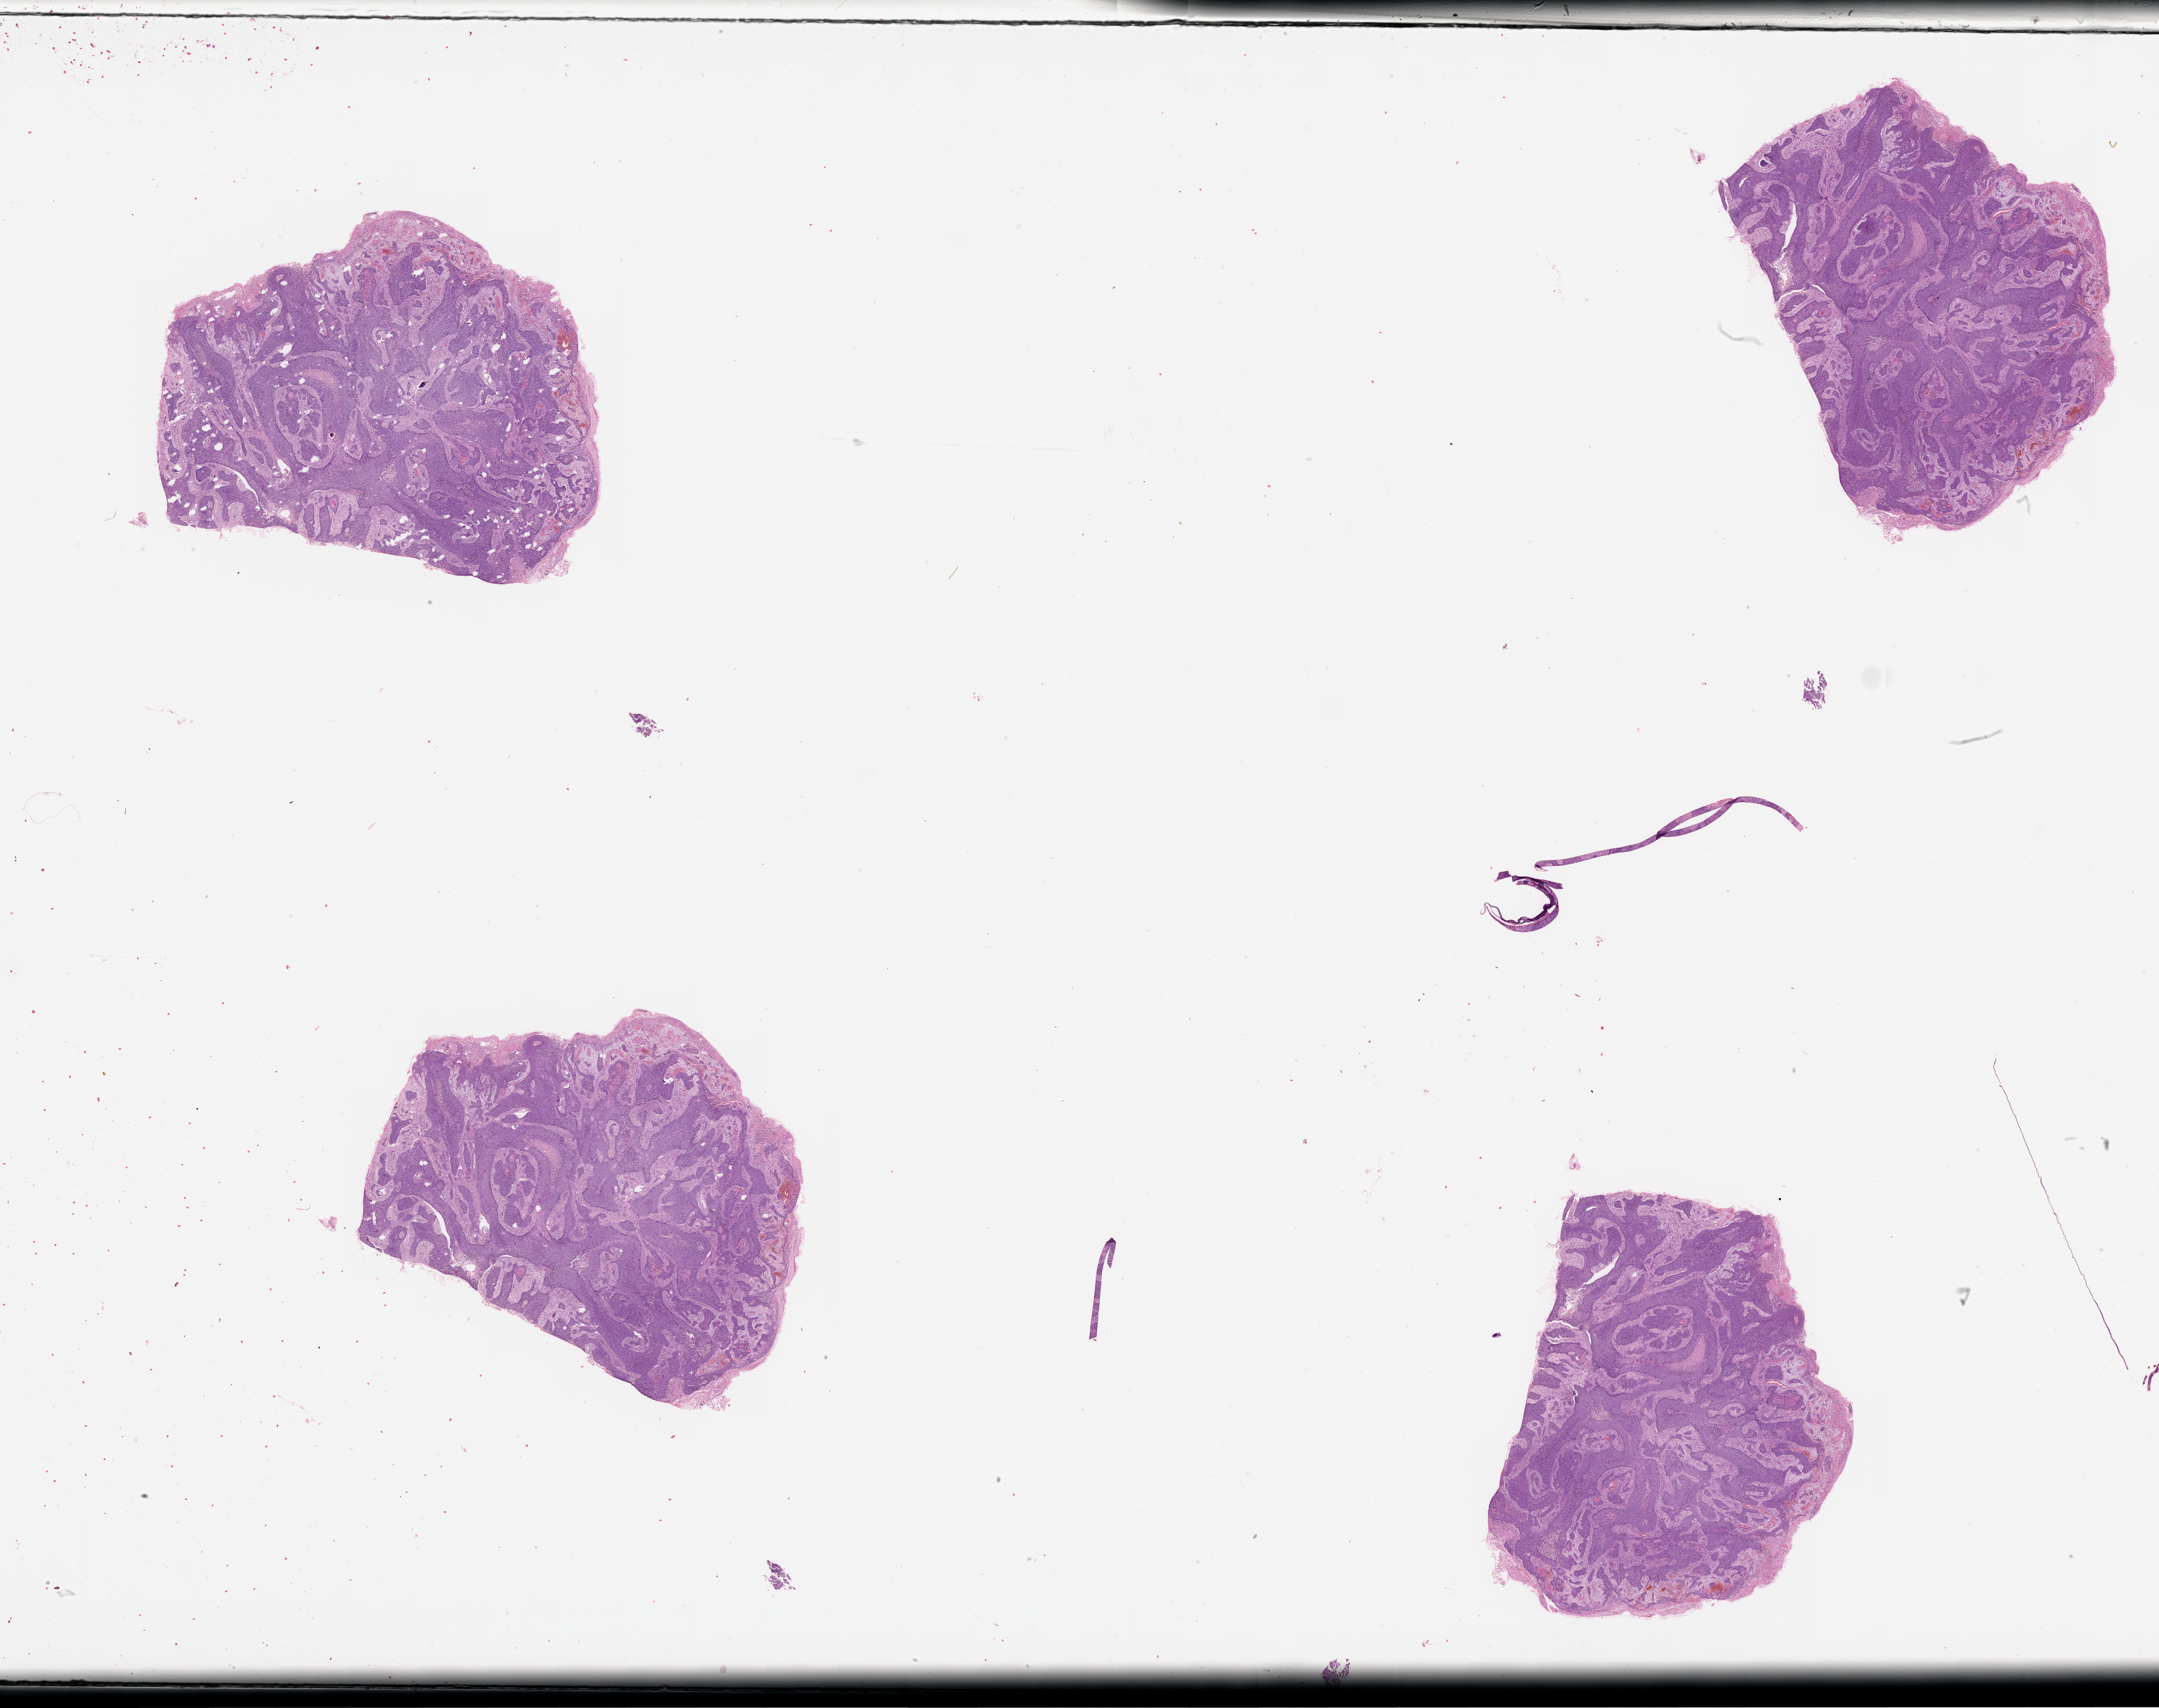
H&E-stained whole-slide image — a low-resolution overview of the entire scanned area, about 31.1 x 24.6 mm (acquisition: 20x scan), tumour tissue sample, lung. 59-year-old male patient.
• patient diagnosis (cohort enrolment): squamous cell carcinoma (lung)